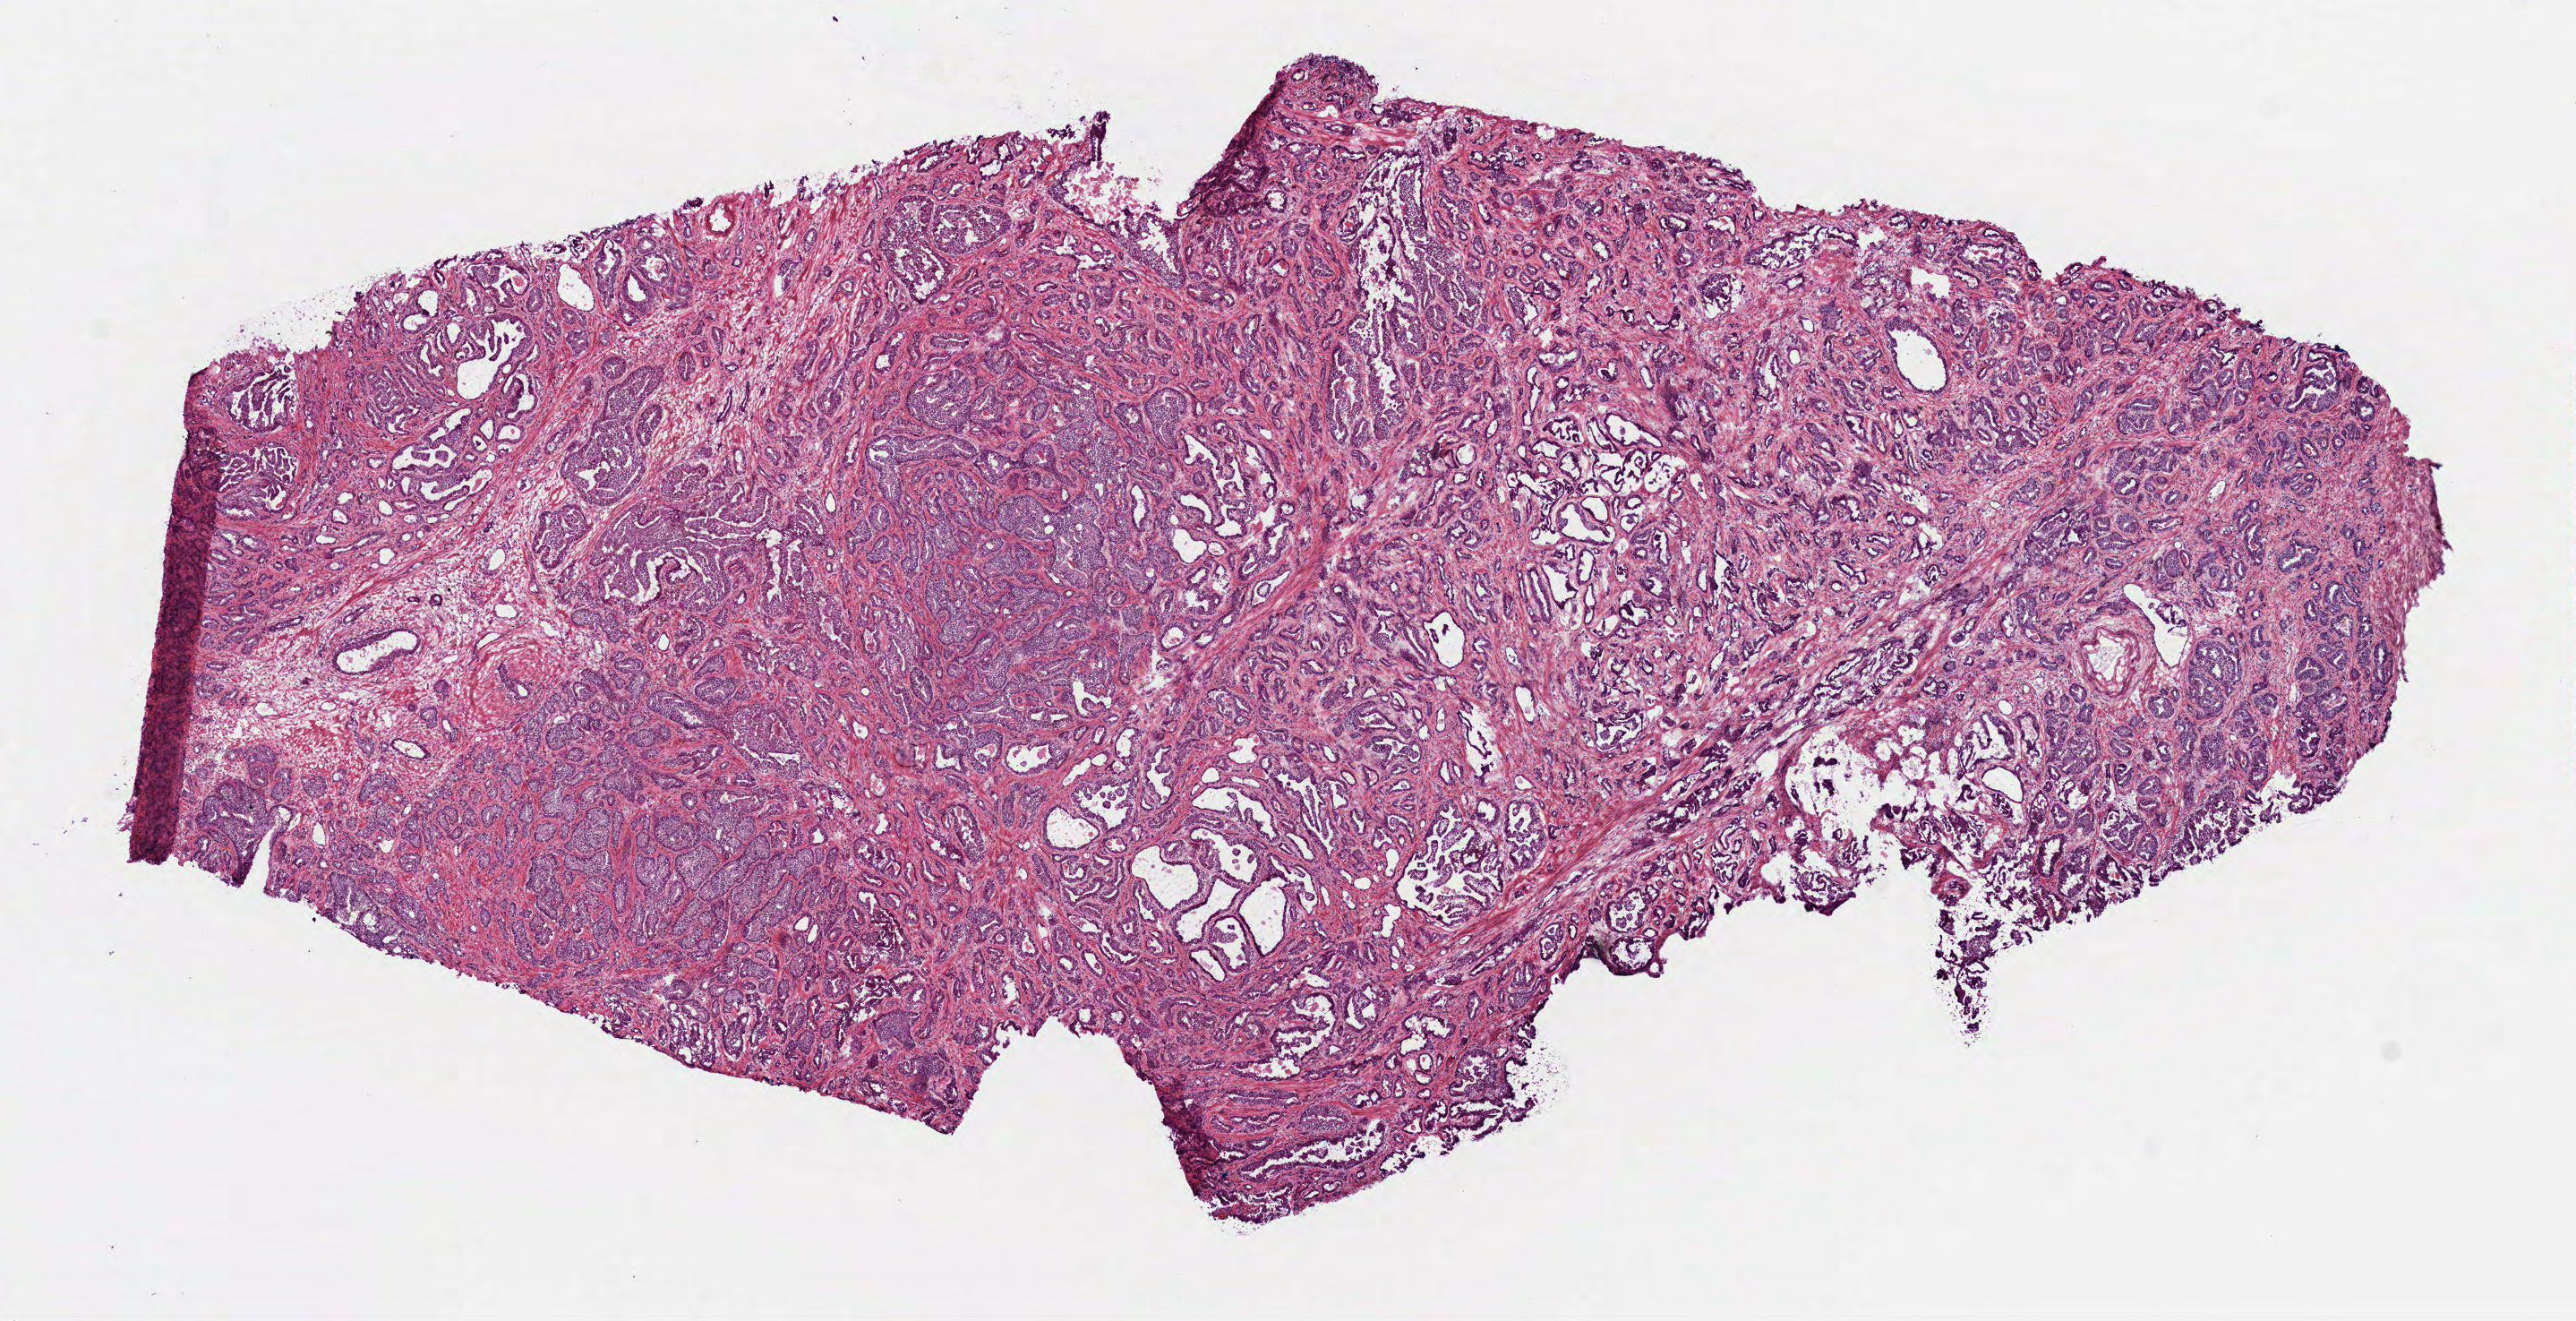
Hematoxylin and eosin (H&E) stained whole-slide image — shown as a low-resolution overview of the whole scanned area (about 11.6 x 5.9 mm, acquisition: 40x scan). Frozen section from the bottom of the tissue portion. Sample: primary tumour, prostate. Male patient; age at initial diagnosis 64 years. Composition of this section per pathologist review: tumour cells 80%, tumour nuclei 80%.
Histologic diagnosis: Acinar cell carcinoma (prostate gland).